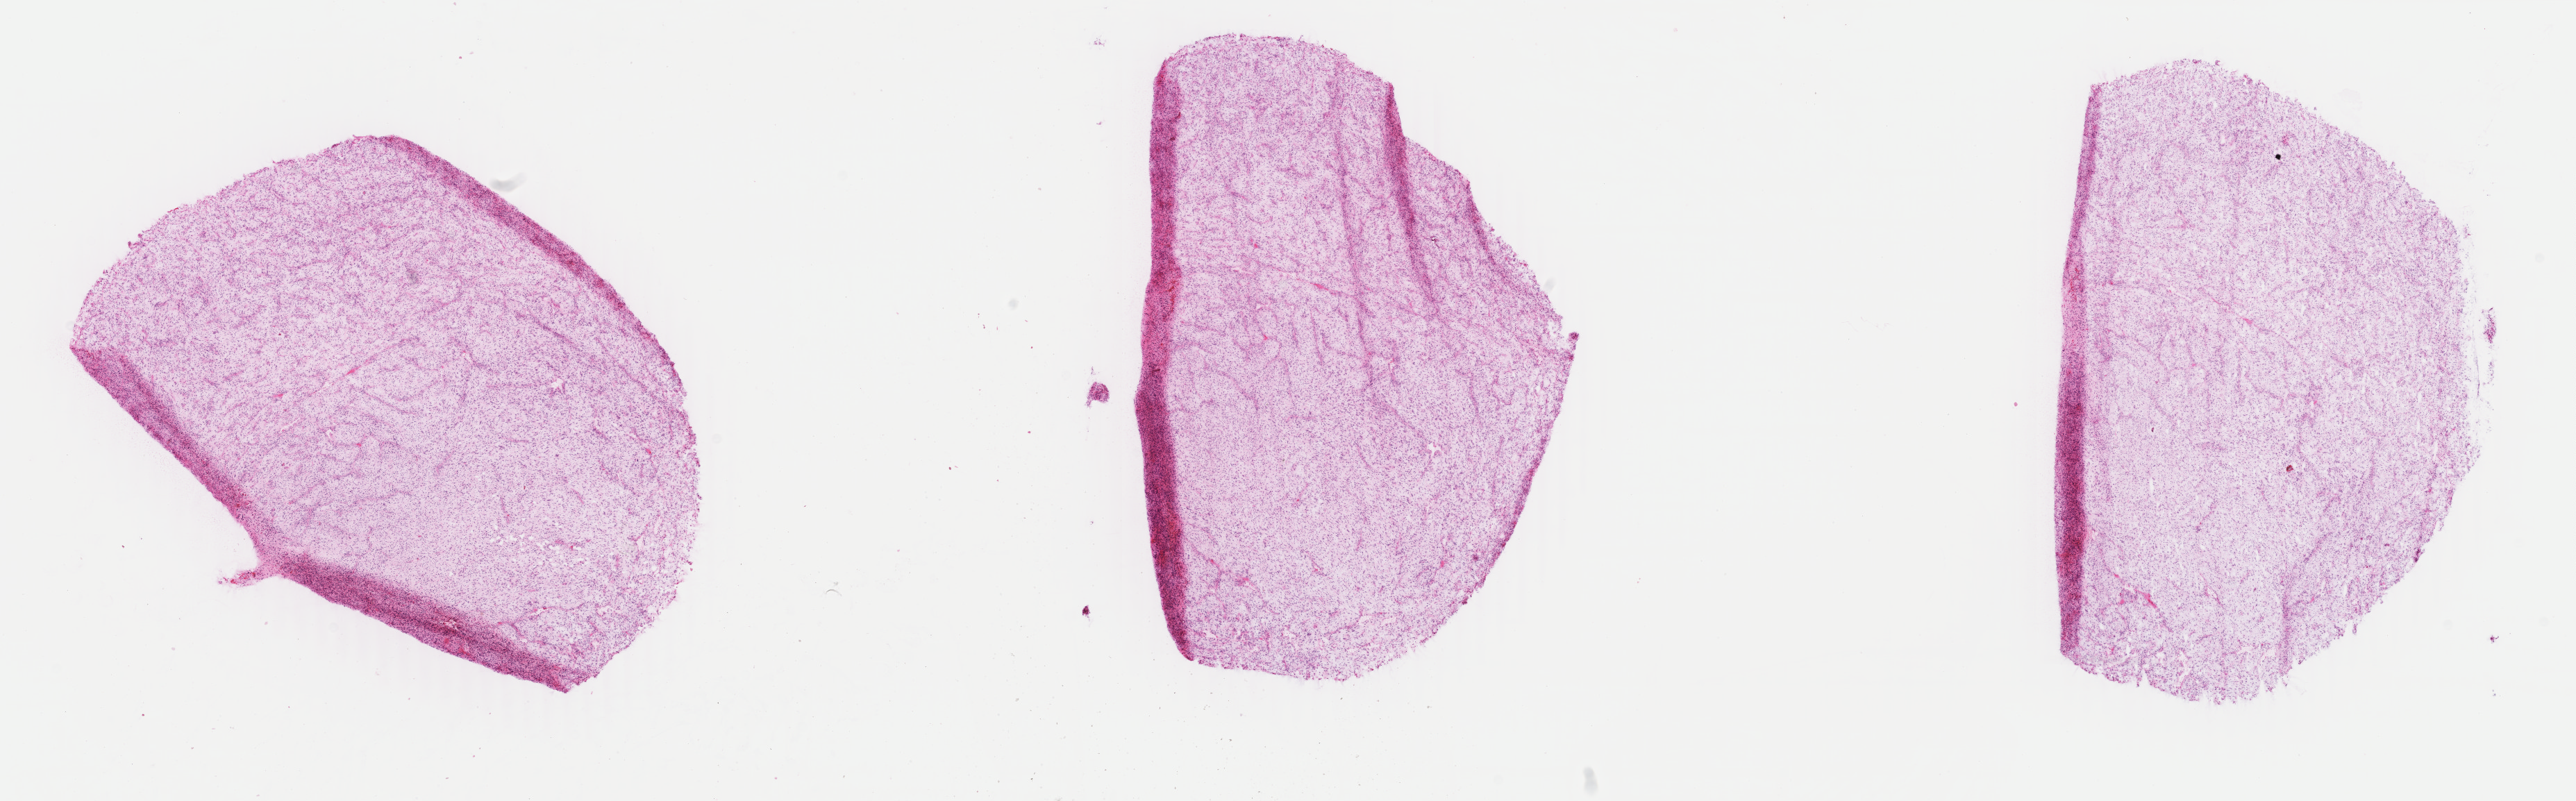
Whole-slide histology image, Hematoxylin and eosin (H&E) stained, shown as a low-resolution overview of the whole scanned area (about 29.5 x 9.2 mm), formalin-fixed paraffin-embedded (FFPE) diagnostic section, sample: primary tumour, kidney. Patient: male, age at initial diagnosis 75 years.
• pathologic diagnosis: Giant cell sarcoma